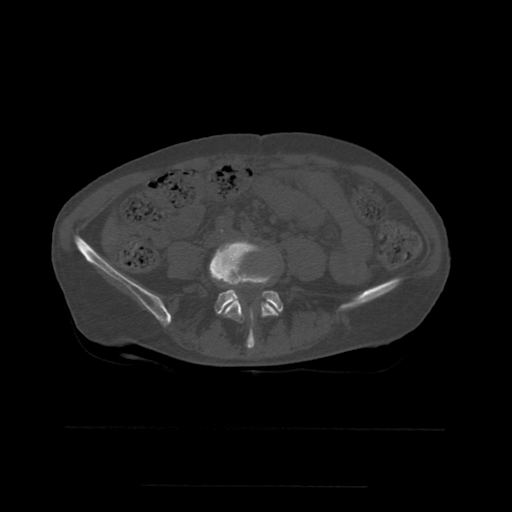
CT including the spine, one axial slice. Position 156 of 544 along the scan axis. Bone window (W 1800 / L 400 HU). 512 × 512 image matrix. Patient age 58 years. From the clinical record (not read from this slice): primary cancer: lung.
Structures marked on this image (semi-automatically segmented with operator editing):
- L4 vertebra: bounding box [x1, y1, x2, y2] px = [211, 240, 279, 349]
- L5 vertebra: [210, 260, 284, 319]